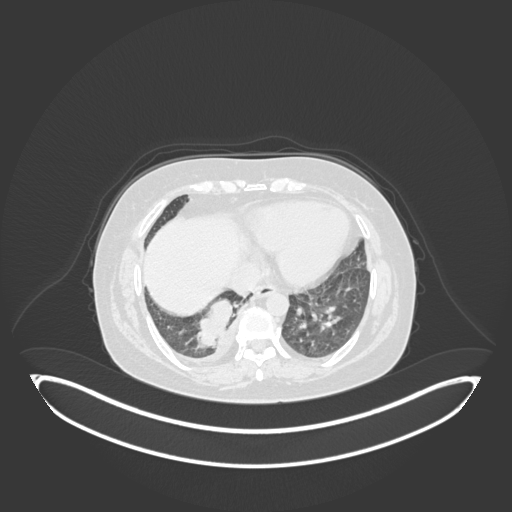
Chest CT, one axial slice; position 40 of 231 along the scan axis; reconstruction kernel B30f; lung window (W 1500 / L -600 HU); 1 mm slice thickness; 512 × 512 image matrix. Patient: female, 56 years. From the clinical record (not read from this slice): clinical TNM (as recorded): T2b N1 M0; histopathological grade: G3.
Outlined on this slice (bounding box drawn by a radiologist):
- lung tumour (recorded histology: small cell carcinoma): box from (x=192, y=299) to (x=236, y=353) px